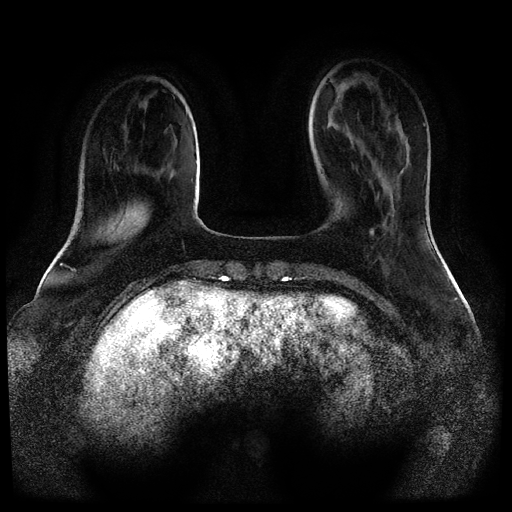
Breast MRI (dynamic contrast-enhanced, multi-phase), one axial slice. Slice 26 of 116 in the series (ordered by position). Dynamic contrast-enhanced series, time point 2 of 5 at this slice position (early post-contrast). 1.5 T. TE 2.6 ms, TR 5.3 ms. 2 mm slice thickness. 512 × 512 image matrix, field of view 360 × 360 mm. Patient: female, 52 years.
Annotated regions visible in this slice (semi-automatic segmentation, software-assisted and operator-edited):
- breast lesion (labelled 'tumour' in the annotation; benign lesions carry a separate 'benign' label): box from (x=369, y=229) to (x=374, y=236) px